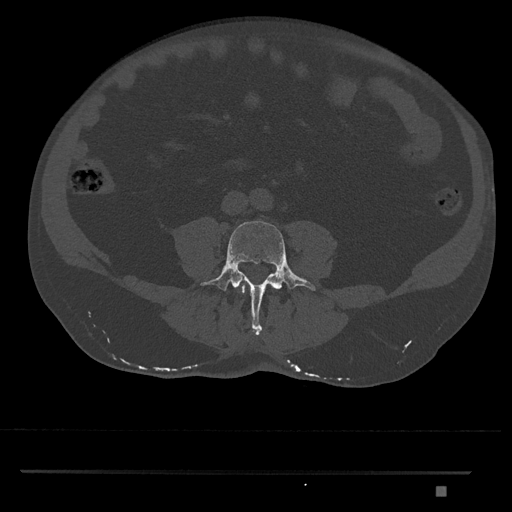
CT including the spine, one axial slice. Slice 621 of 1134 in the series (ordered by position). 120 kVp. Bone window (W 1800 / L 400 HU). 0.5 mm slice thickness. 512 × 512 image matrix, field of view 429 × 429 mm. Male patient, age 65 years. From the clinical record (not read from this slice): primary cancer: prostate.
Structures marked on this image (semi-automatic segmentation, software-assisted and operator-edited):
- L3 vertebra: bounding box <241,285,245,294> (left, top, right, bottom; pixels)
- L4 vertebra: <200,221,316,335>